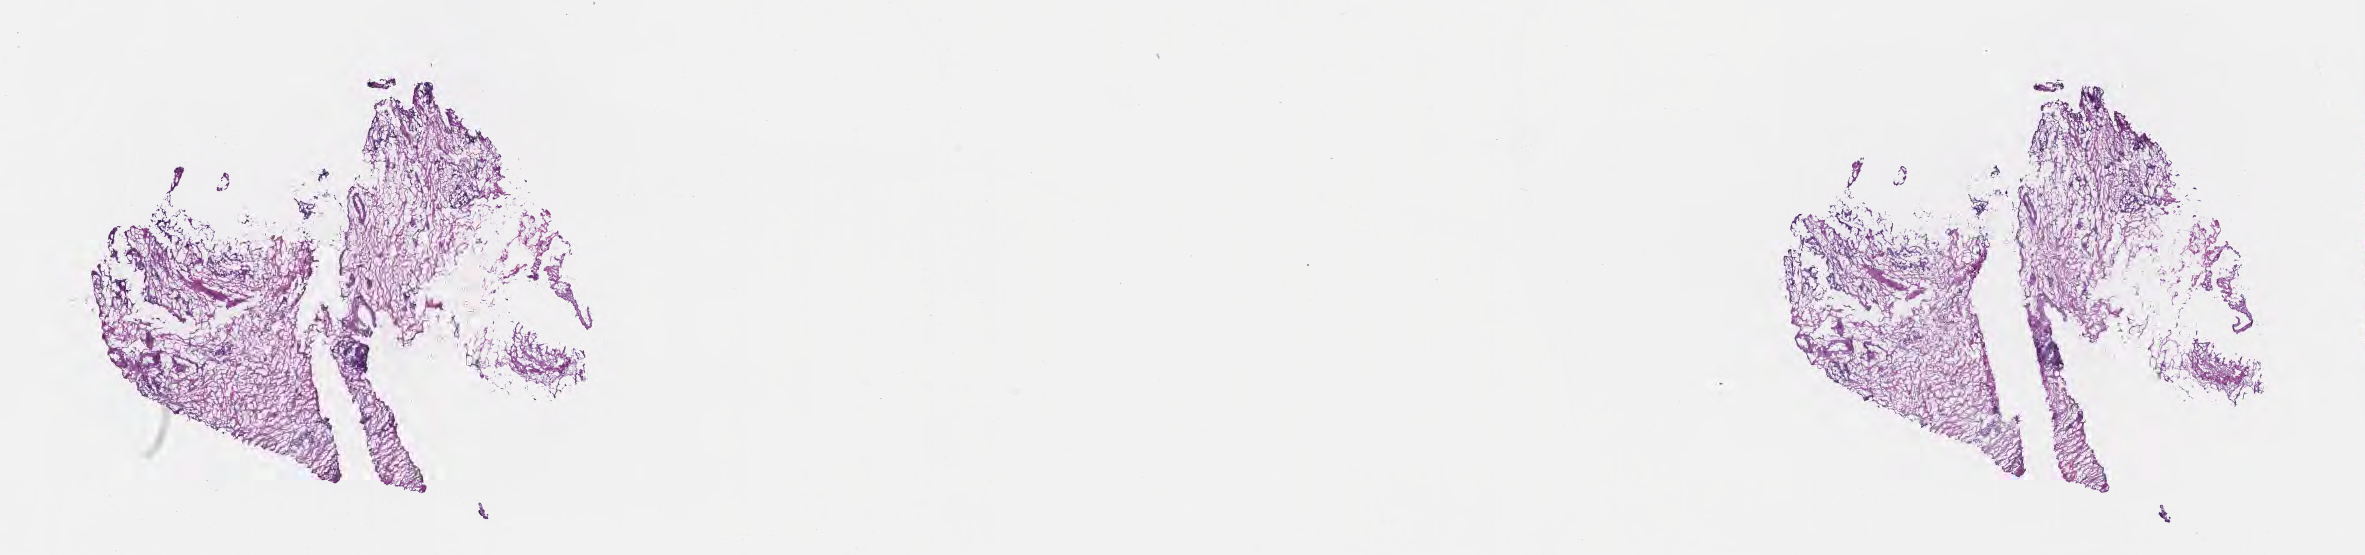
Haematoxylin and eosin whole-slide image — low-resolution overview of the scanned area, about 19.1 x 4.5 mm; cryosection; primary tumor; anatomic site: body of pancreas. Patient: female, age at initial diagnosis 64 years. Slide review estimates, as recorded: tumor cells 50%, tumor nuclei 15%, stromal cells 50%, necrosis 0%, normal cells 0%. Inflammatory infiltration, as recorded: lymphocyte infiltration 0%, monocyte infiltration 0%, neutrophil infiltration 0%.
Section: top of the tissue portion. AJCC pathologic stage: Stage IIB. Diagnosis: Adenocarcinoma, NOS.